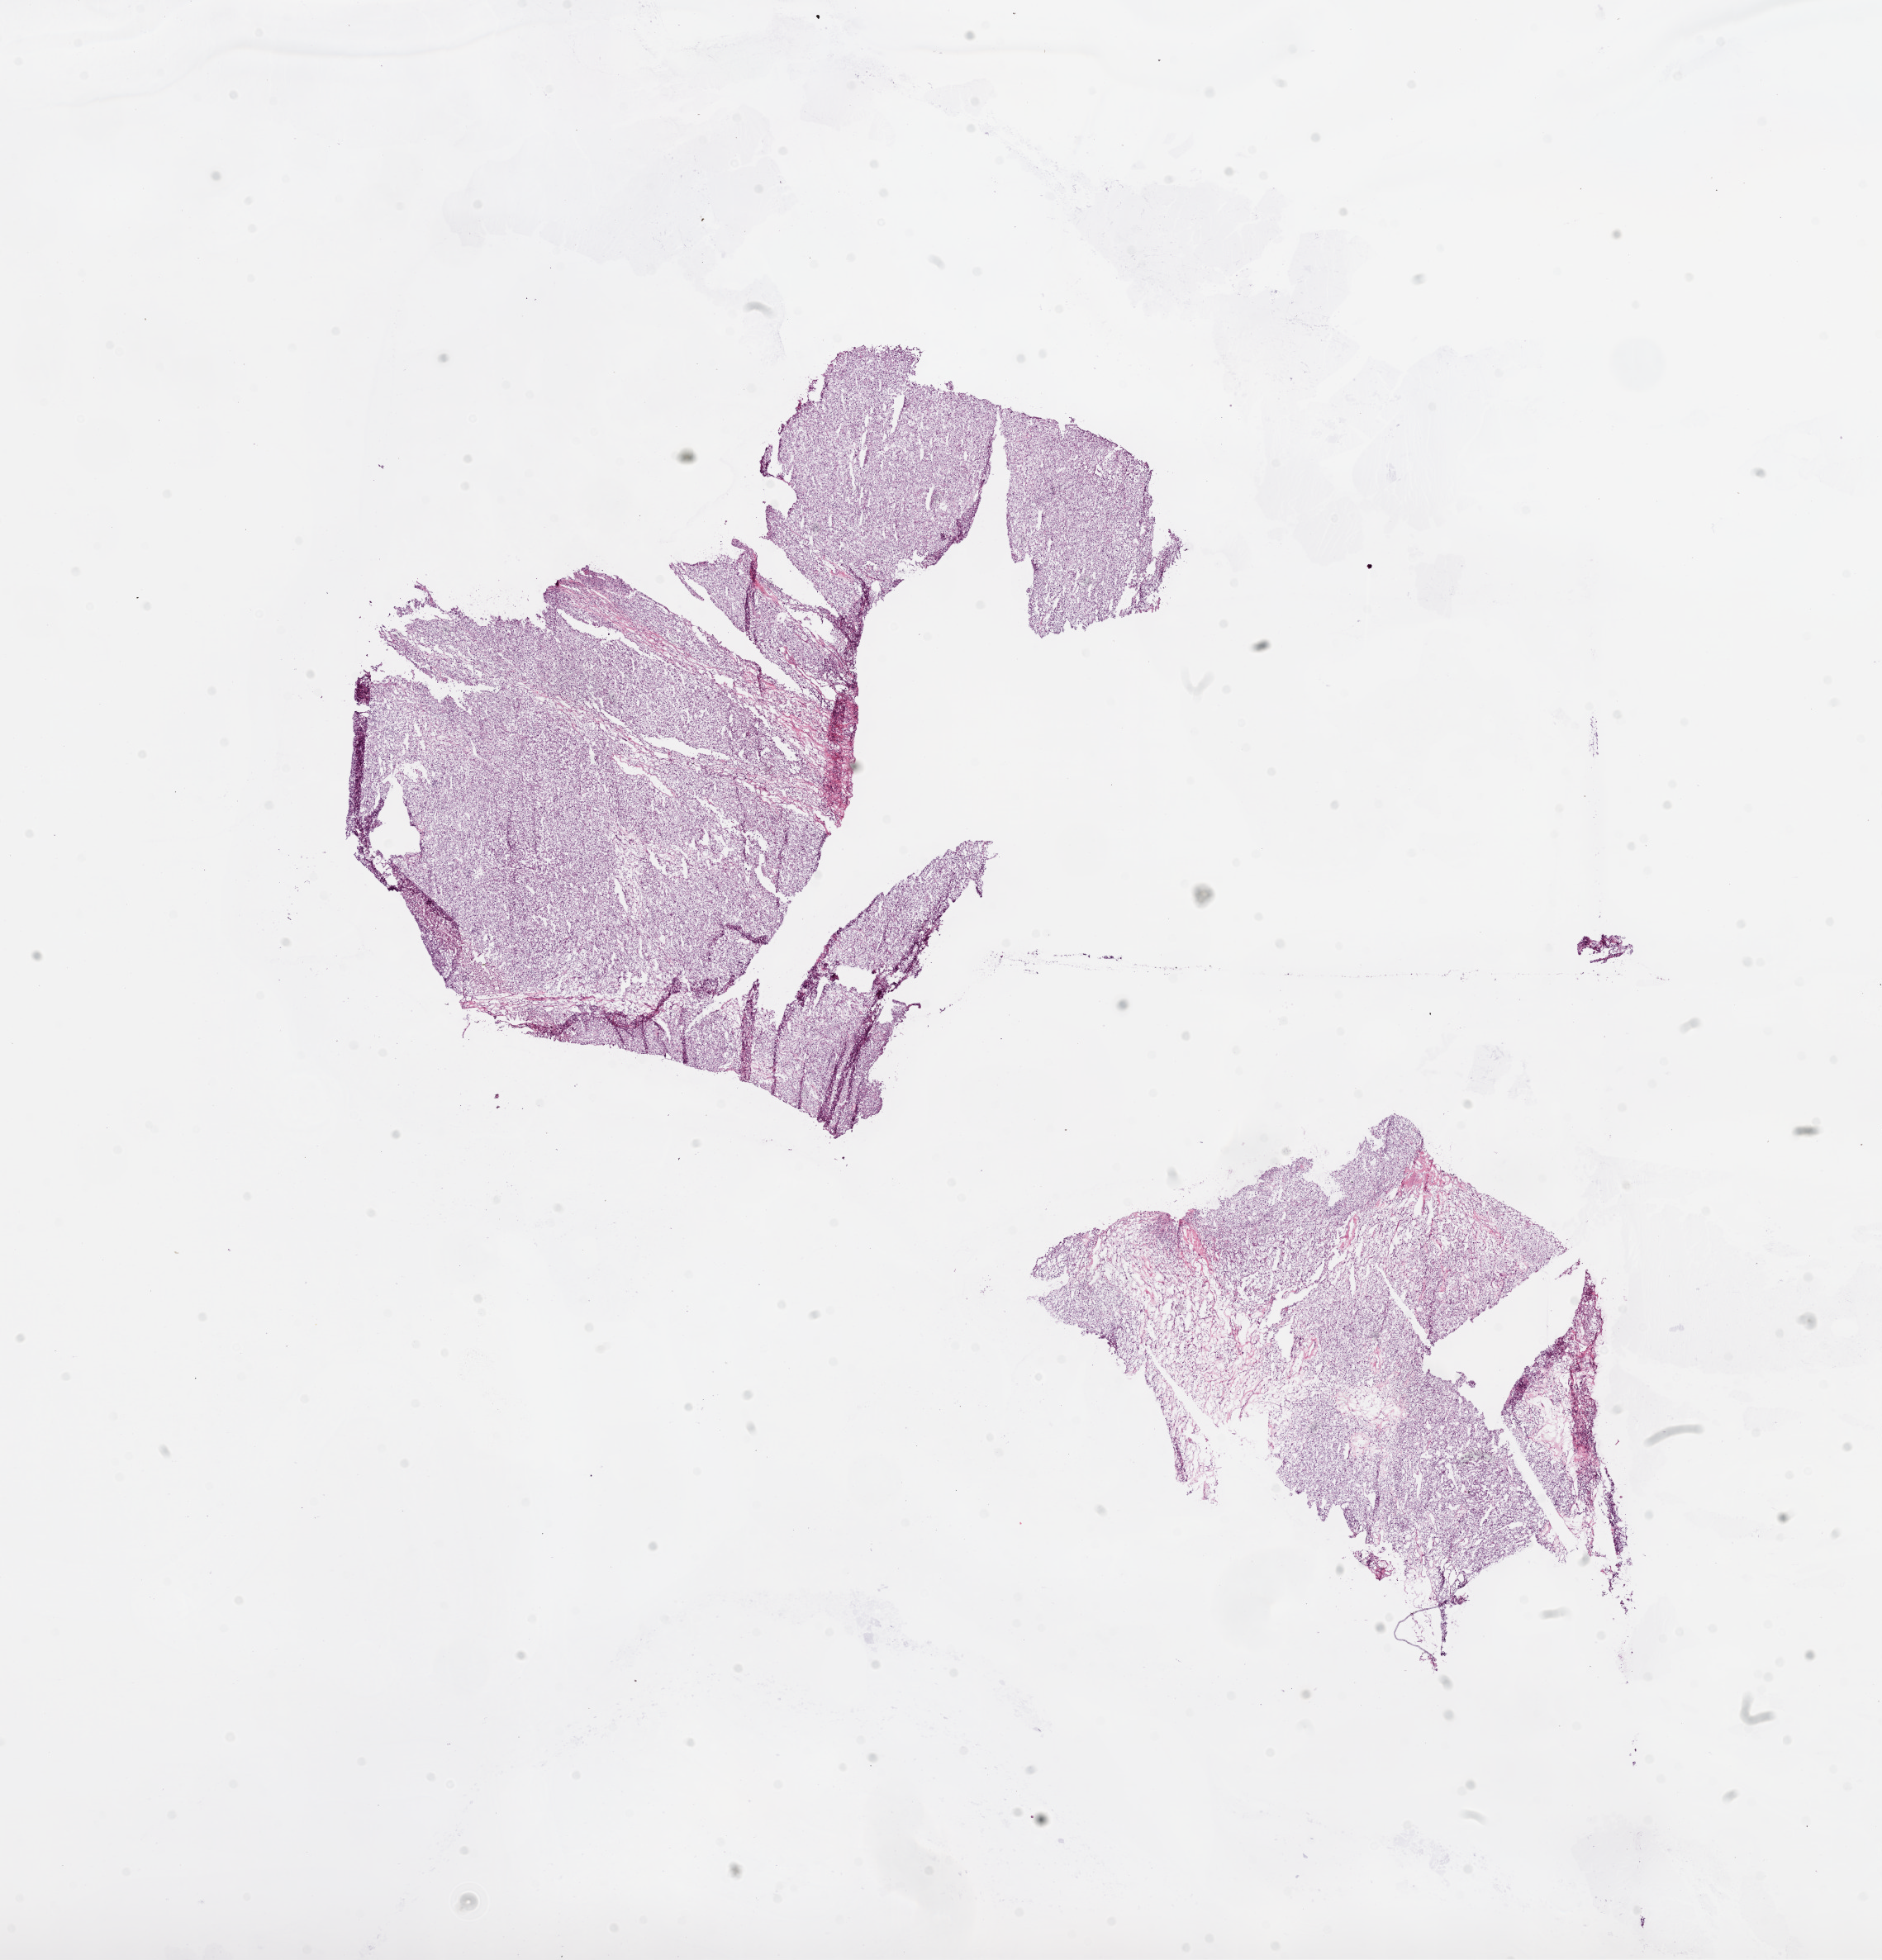
Whole-slide histology image, H&E-stained, a low-resolution overview of the entire scanned area, about 18.4 x 19.1 mm (slide scanned at 20x). Frozen section from the top of the tissue portion. Primary tumour sample from the kidney. Male patient; age at initial diagnosis 53 years. Histologic grade: G3 (poorly differentiated). Composition of this section per pathologist review: tumour cells 90%, tumour nuclei 85%, normal cells 0%, stromal cells 10%, necrosis 0%.
- diagnosis: Clear cell adenocarcinoma, NOS
- TNM: T1b NX M0
- AJCC pathologic stage: I (6th edition)